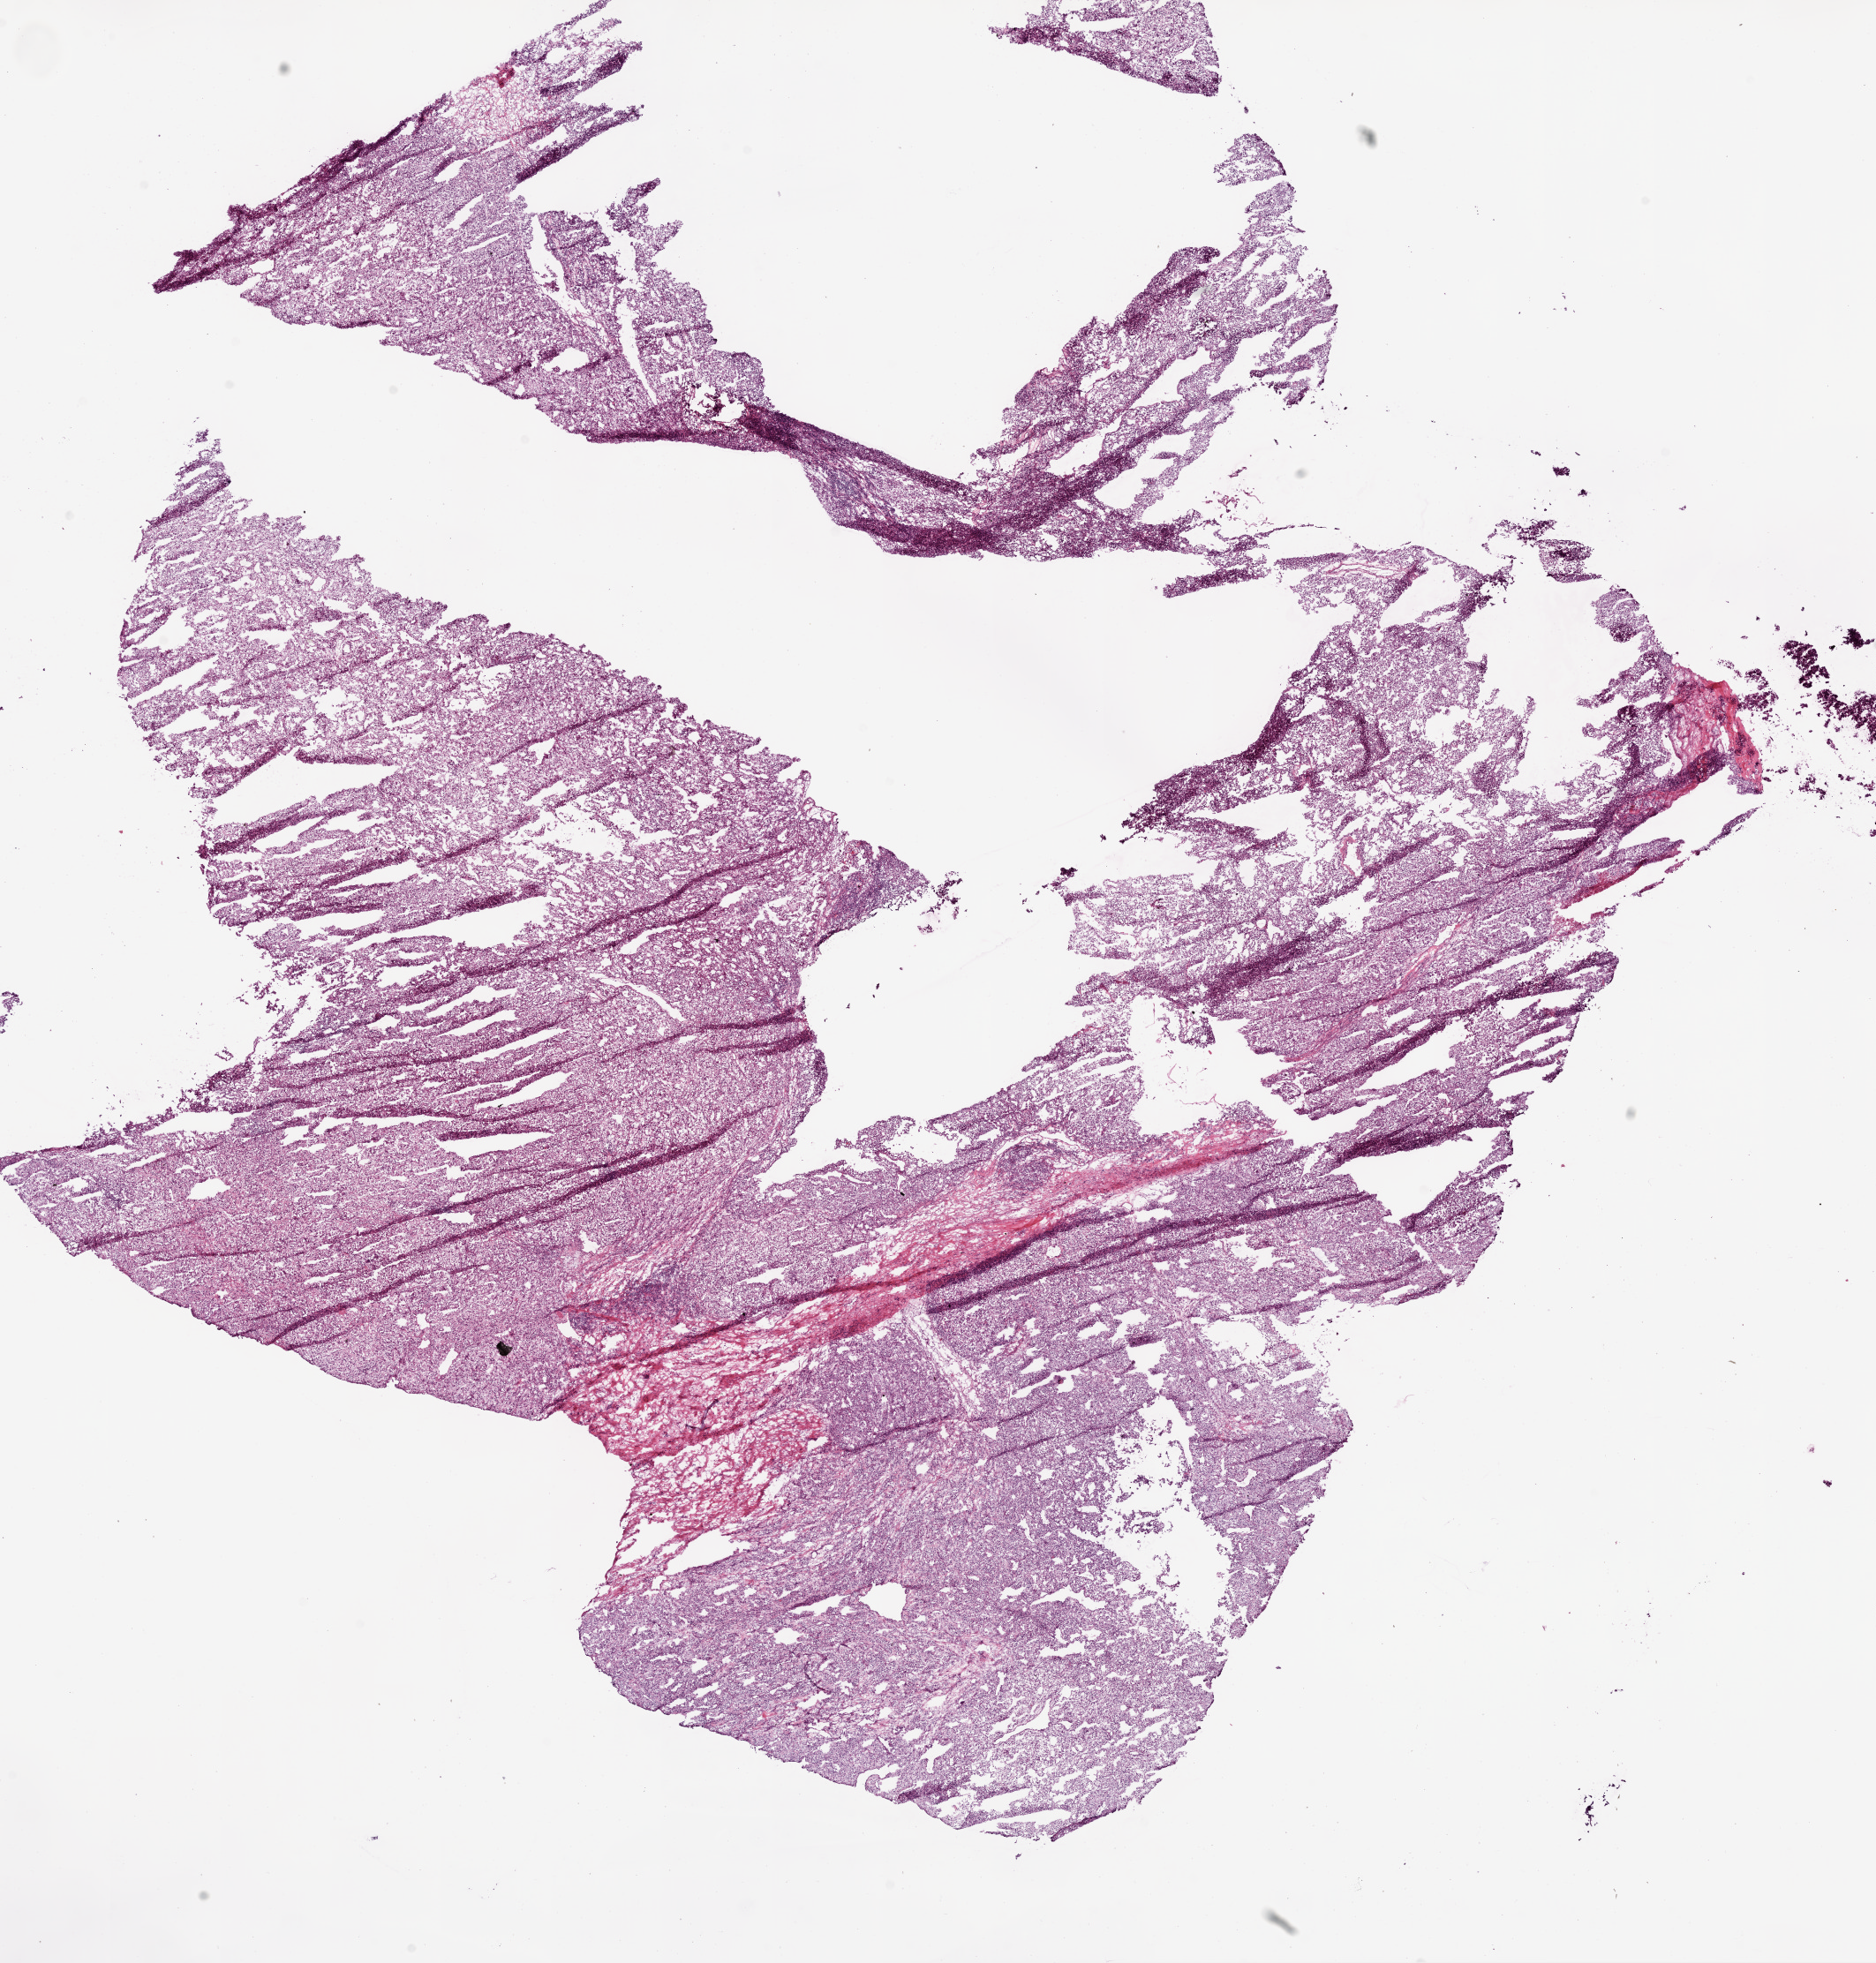
H&E-stained whole-slide image, a low-resolution overview of the entire scanned area, about 17.1 x 17.8 mm (slide scanned at 20x). Frozen section from the bottom of the tissue portion. Kidney, primary tumour sample. Male patient; age at initial diagnosis 68 years. Composition of this section per pathologist review: tumour cells 90%, tumour nuclei 90%.
Histologic diagnosis: Clear cell adenocarcinoma, NOS.